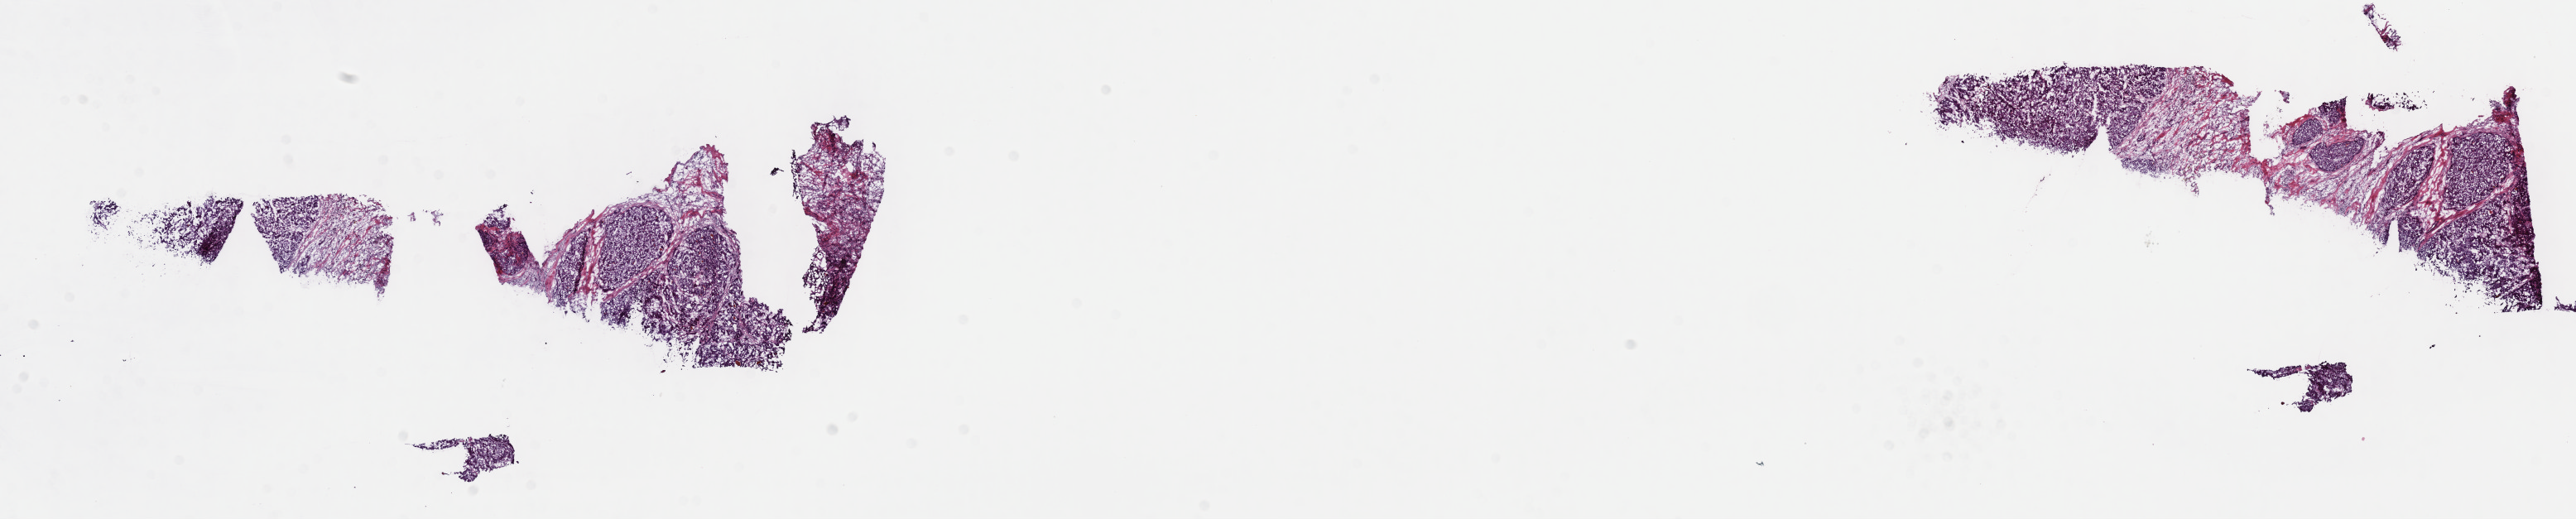
Digitized H&E tissue section (whole slide), whole scanned area (about 25.2 x 5.1 mm, from a 40x scan) shown as a low-resolution overview; frozen section from the top of the tissue portion; liver, primary tumour sample. Patient: male, age at initial diagnosis 66 years. Histologic grade: G2 (moderately differentiated). Composition of this section per pathologist review: tumour cells 42%, tumour nuclei 80%, normal cells 0%, stromal cells 55%, necrosis 3%. Inflammatory infiltration, as recorded: lymphocyte infiltration 12%, monocyte infiltration 1%, neutrophil infiltration 2%.
TNM: T1 N0 M0. AJCC pathologic stage: I (7th edition). Diagnosis: Hepatocellular carcinoma, NOS.